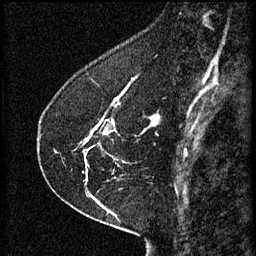
Breast MRI (dynamic contrast-enhanced), one sagittal slice; position 20 of 60 along the scan axis; 3 images stored at this slice position (order not interpretable as contrast timing); 1.5 T; TE 4.2 ms, TR 8.2 ms; 2 mm slice thickness; 256 × 256 image matrix. Patient: female, 41 years.
Annotated regions visible in this slice (semi-automatically segmented with operator editing):
- analysis volume of interest (the breast-tissue region the enhancement analysis was run in; not a lesion): bounding box (x1, y1, x2, y2) in pixels: (77, 116, 153, 173)
- tumour enhancement mask (voxels above the 70 % enhancement threshold inside the analysis volume of interest): (84, 118, 153, 143)